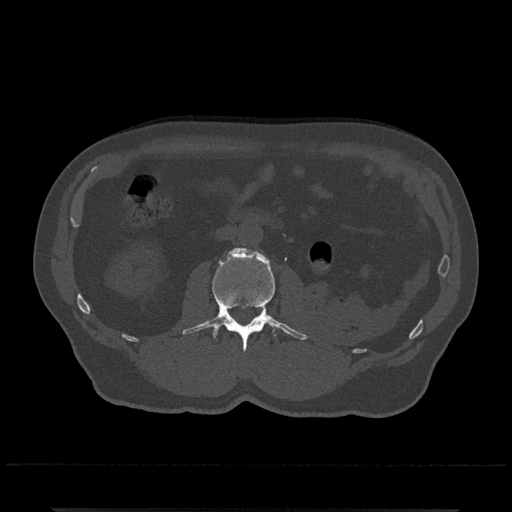
CT including the spine, one axial slice; position 289 of 797 along the scan axis; reconstruction kernel Br40s/3; bone window (W 1800 / L 400 HU); 0.5 mm slice thickness; 512 × 512 image matrix, field of view 393 × 393 mm. Patient: male, 67 years. Case-level facts recorded for this patient, not image findings: primary cancer: prostate.
Structures marked on this image (semi-automatic segmentation, software-assisted and operator-edited):
- L2 vertebra: box from (x=182, y=248) to (x=308, y=352) px